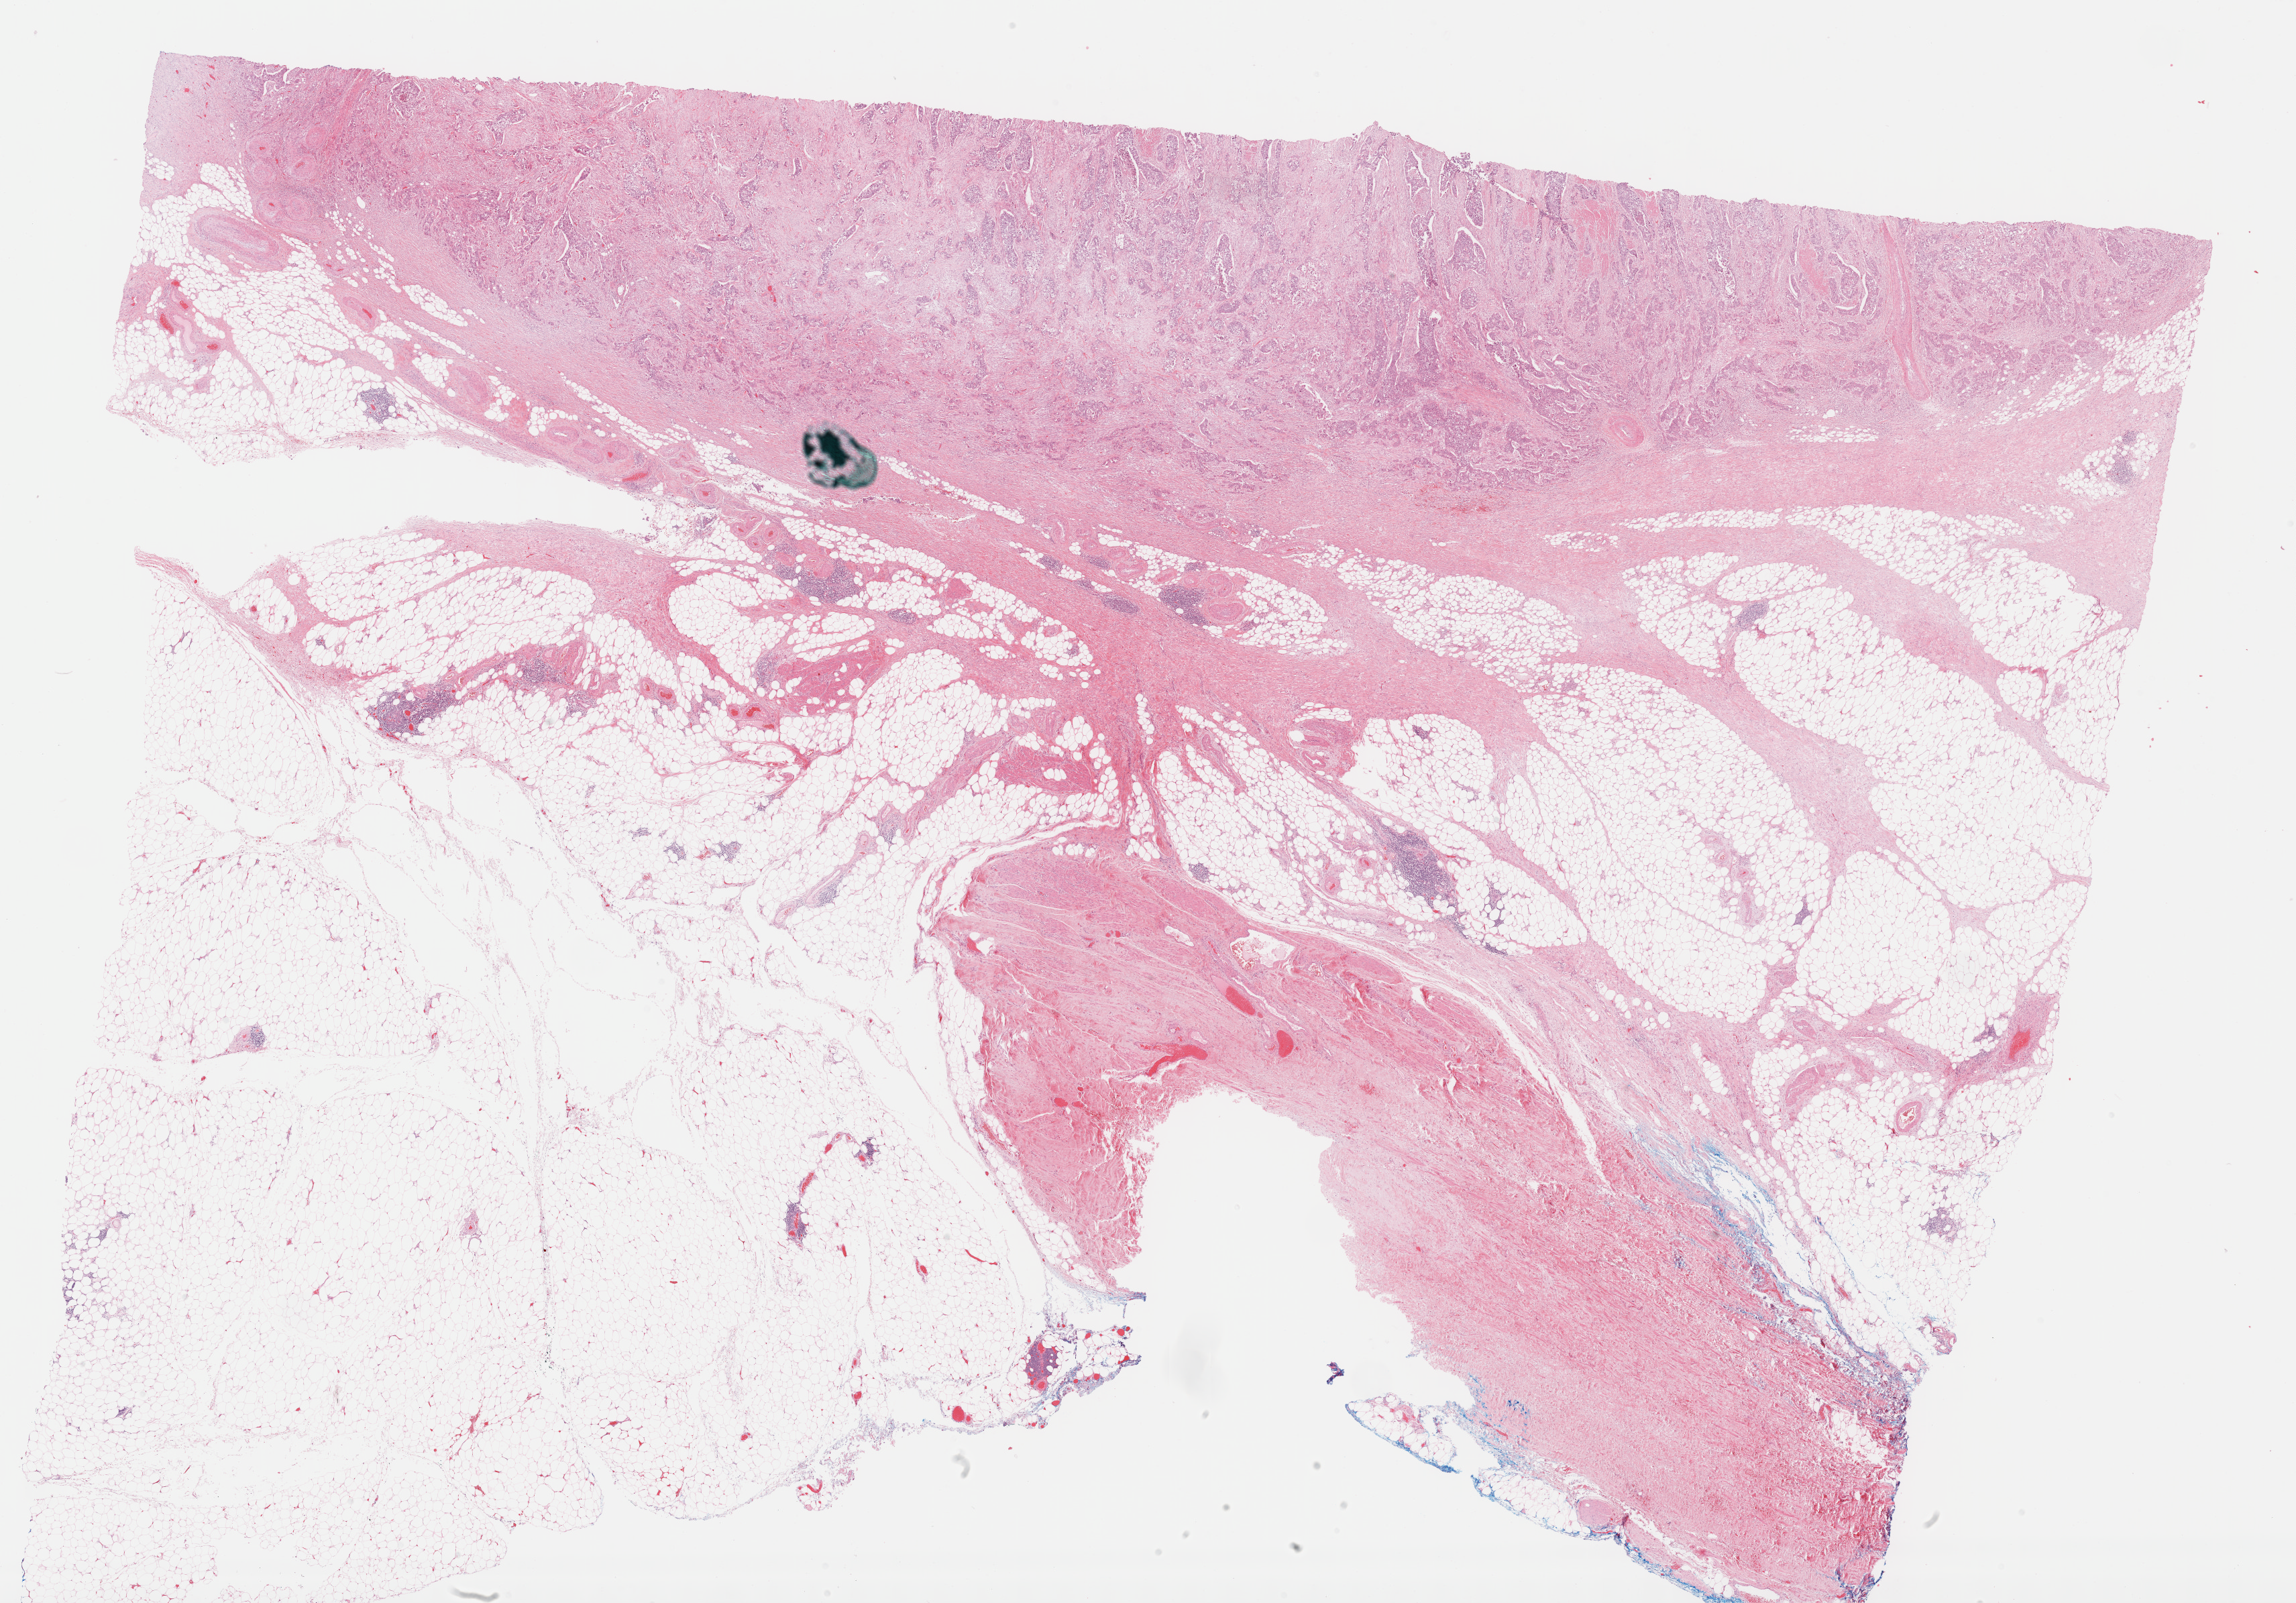
H&E whole-slide image, shown as a low-resolution overview of the whole scanned area (about 27.7 x 19.3 mm, slide scanned at 40x), formalin-fixed paraffin-embedded (FFPE) diagnostic section, bladder, primary tumour sample. Male, age 77 years at initial diagnosis. Histologic grade: high grade.
AJCC pathologic stage: III (6th edition). Diagnosis: Transitional cell carcinoma (lateral wall of bladder). TNM: T3a N0 MX.